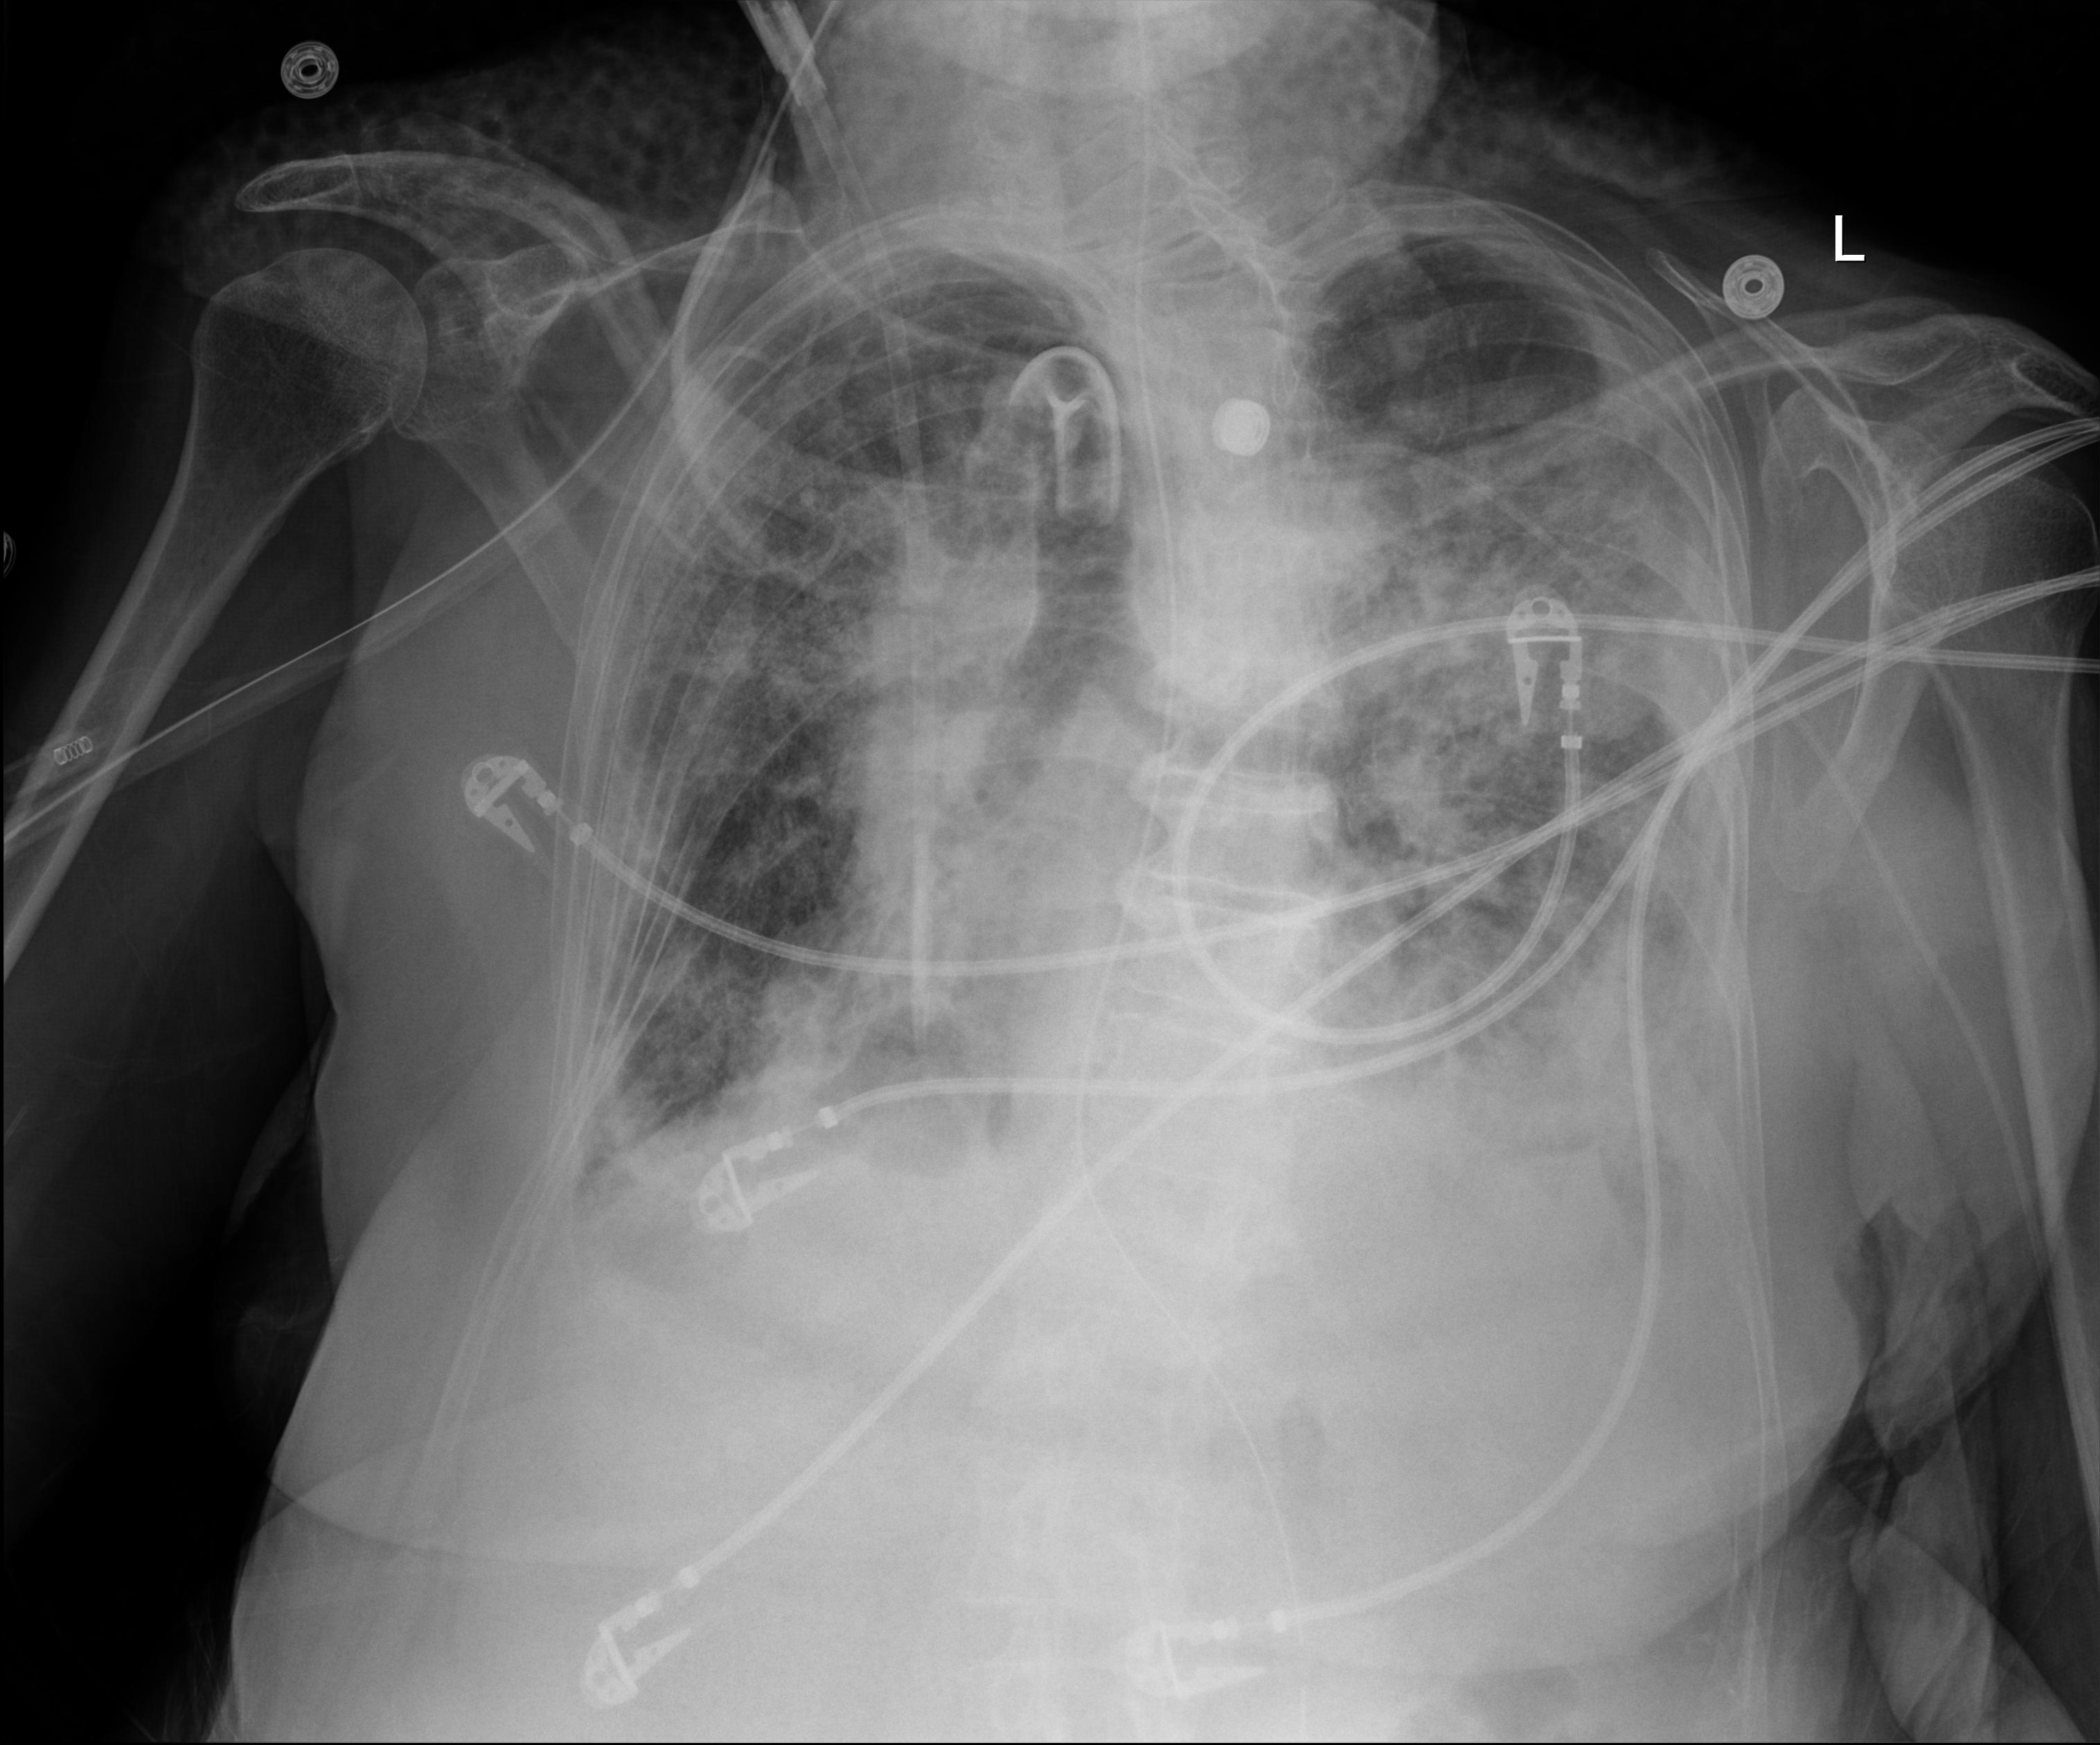
Chest X-ray (portable); anteroposterior (AP) projection. Patient hospitalised with COVID-19; female, aged 75–90 years.
From the hospital-stay record, not from the radiograph (when in the stay this image was taken is not recorded): length of hospital stay: 70 days.